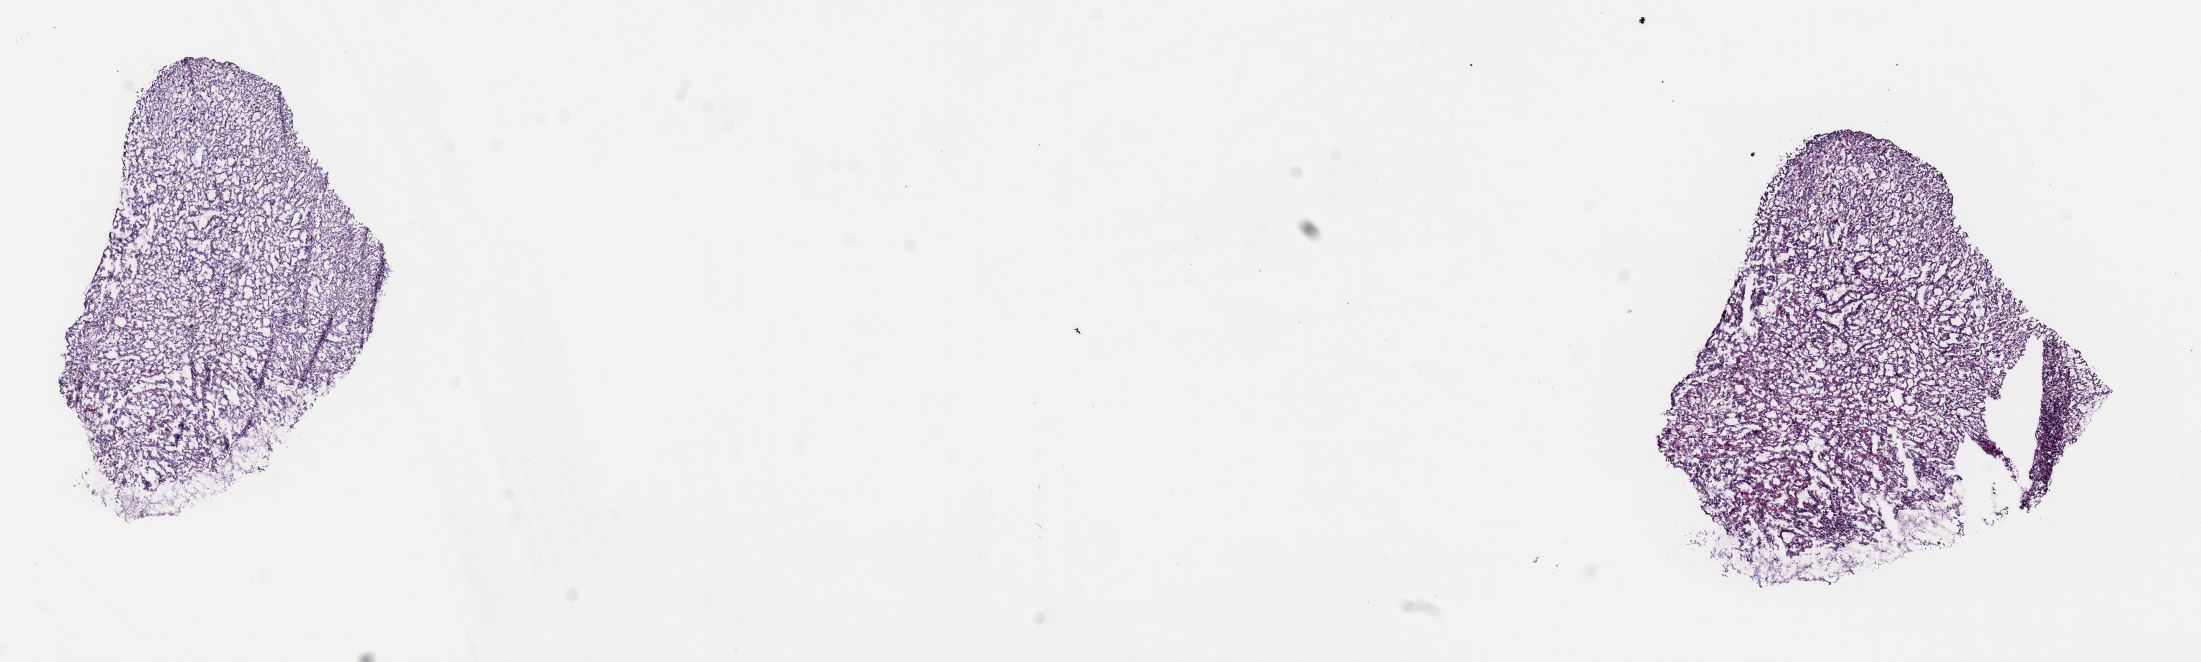
Whole-slide histology image, Hematoxylin and eosin (H&E) stained — low-resolution overview of the scanned area, about 17.4 x 5.2 mm, frozen section from the top of the tissue portion, primary tumour sample from the stomach. Male, age 45 years at initial diagnosis. Histologic grade: G3 (poorly differentiated). Slide review estimates, as recorded: tumour cells 80%, tumour nuclei 80%, normal cells 0%, stromal cells 20%, necrosis 0%. Inflammatory infiltration, as recorded: lymphocyte infiltration 3%, monocyte infiltration 1%, neutrophil infiltration 1%.
AJCC pathologic stage: IIB (7th edition). Histologic diagnosis: Carcinoma, diffuse type (gastric antrum).